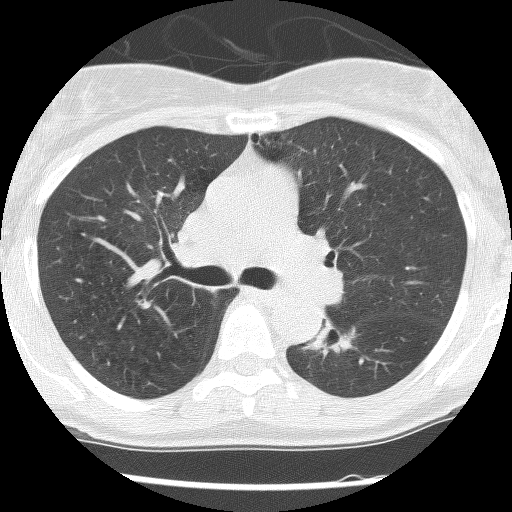
Low-dose screening chest CT, axial slice; second annual screen; lung window (W 1500 / L -600 HU); slice 47 of 120 in the series. Female, age 62 years at enrolment.
- Expert reader's lesion annotation, bounding box (x1, y1, x2, y2) in pixels: (297, 313, 351, 358).
- Screening reader's record for this exam (one nodule recorded; not confirmed to be the boxed lesion): non-calcified nodule or mass ≥4 mm, right upper lobe, 30 × 30 mm, poorly defined margins, ground glass attenuation, pre-existing on the prior screen: yes; interval growth: no.
- Note: the box lies in the patient's left hemithorax on this image, whereas the reader's record names the right lung; they may be different findings.
- Later outcome: lung cancer diagnosed 584 days after this screen (after the third annual screen) — squamous cell carcinoma, NOS, left lower lobe, stage IIIB (AJCC 6th edition), 31 mm at pathology.